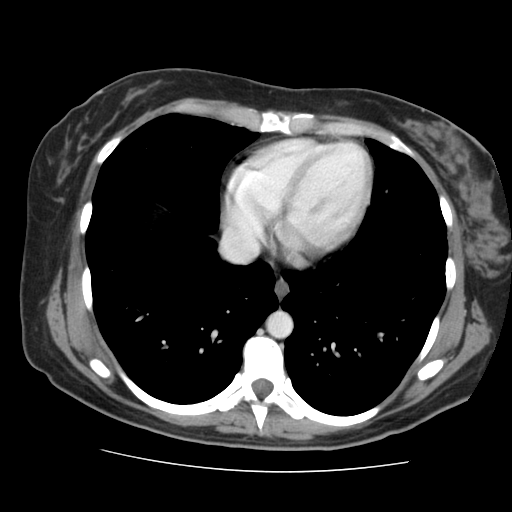
Contrast-enhanced abdominal CT, one axial slice. Slice 141 of 144 in the series (ordered by position). Intravenous contrast given. Soft-tissue window (W 400 / L 40 HU). 2.5 mm slice thickness. 512 × 512 image matrix, field of view 333 × 333 mm. Female patient, age 46 years. Case-level facts recorded for this patient, not image findings: diagnosis: colorectal cancer liver metastases, imaged before liver resection; multiple liver metastases: no.
Outlined on this slice (outlined manually by an expert reader):
- hepatic veins: bounding box <223,238,258,262> (left, top, right, bottom; pixels)